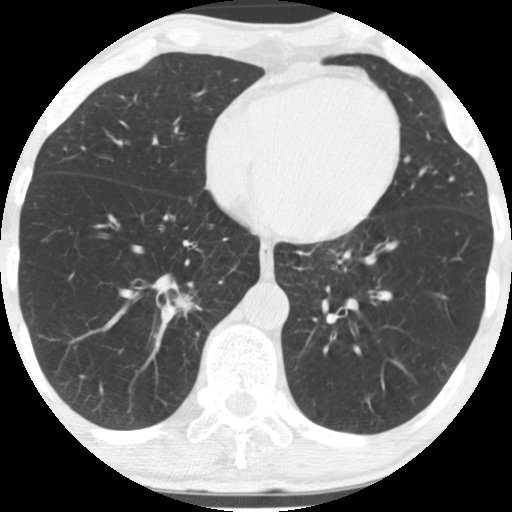
Low-dose screening chest CT, one axial slice. Slice 54 of 170 in the series (ordered by position). 120 kVp. Lung window (W 1500 / L -600 HU). 512 × 512 image matrix.
Outlined on this slice (manually delineated by an expert):
- lesion 1 (tumor, lower lobe of right lung): box from (x=174, y=293) to (x=192, y=310) px